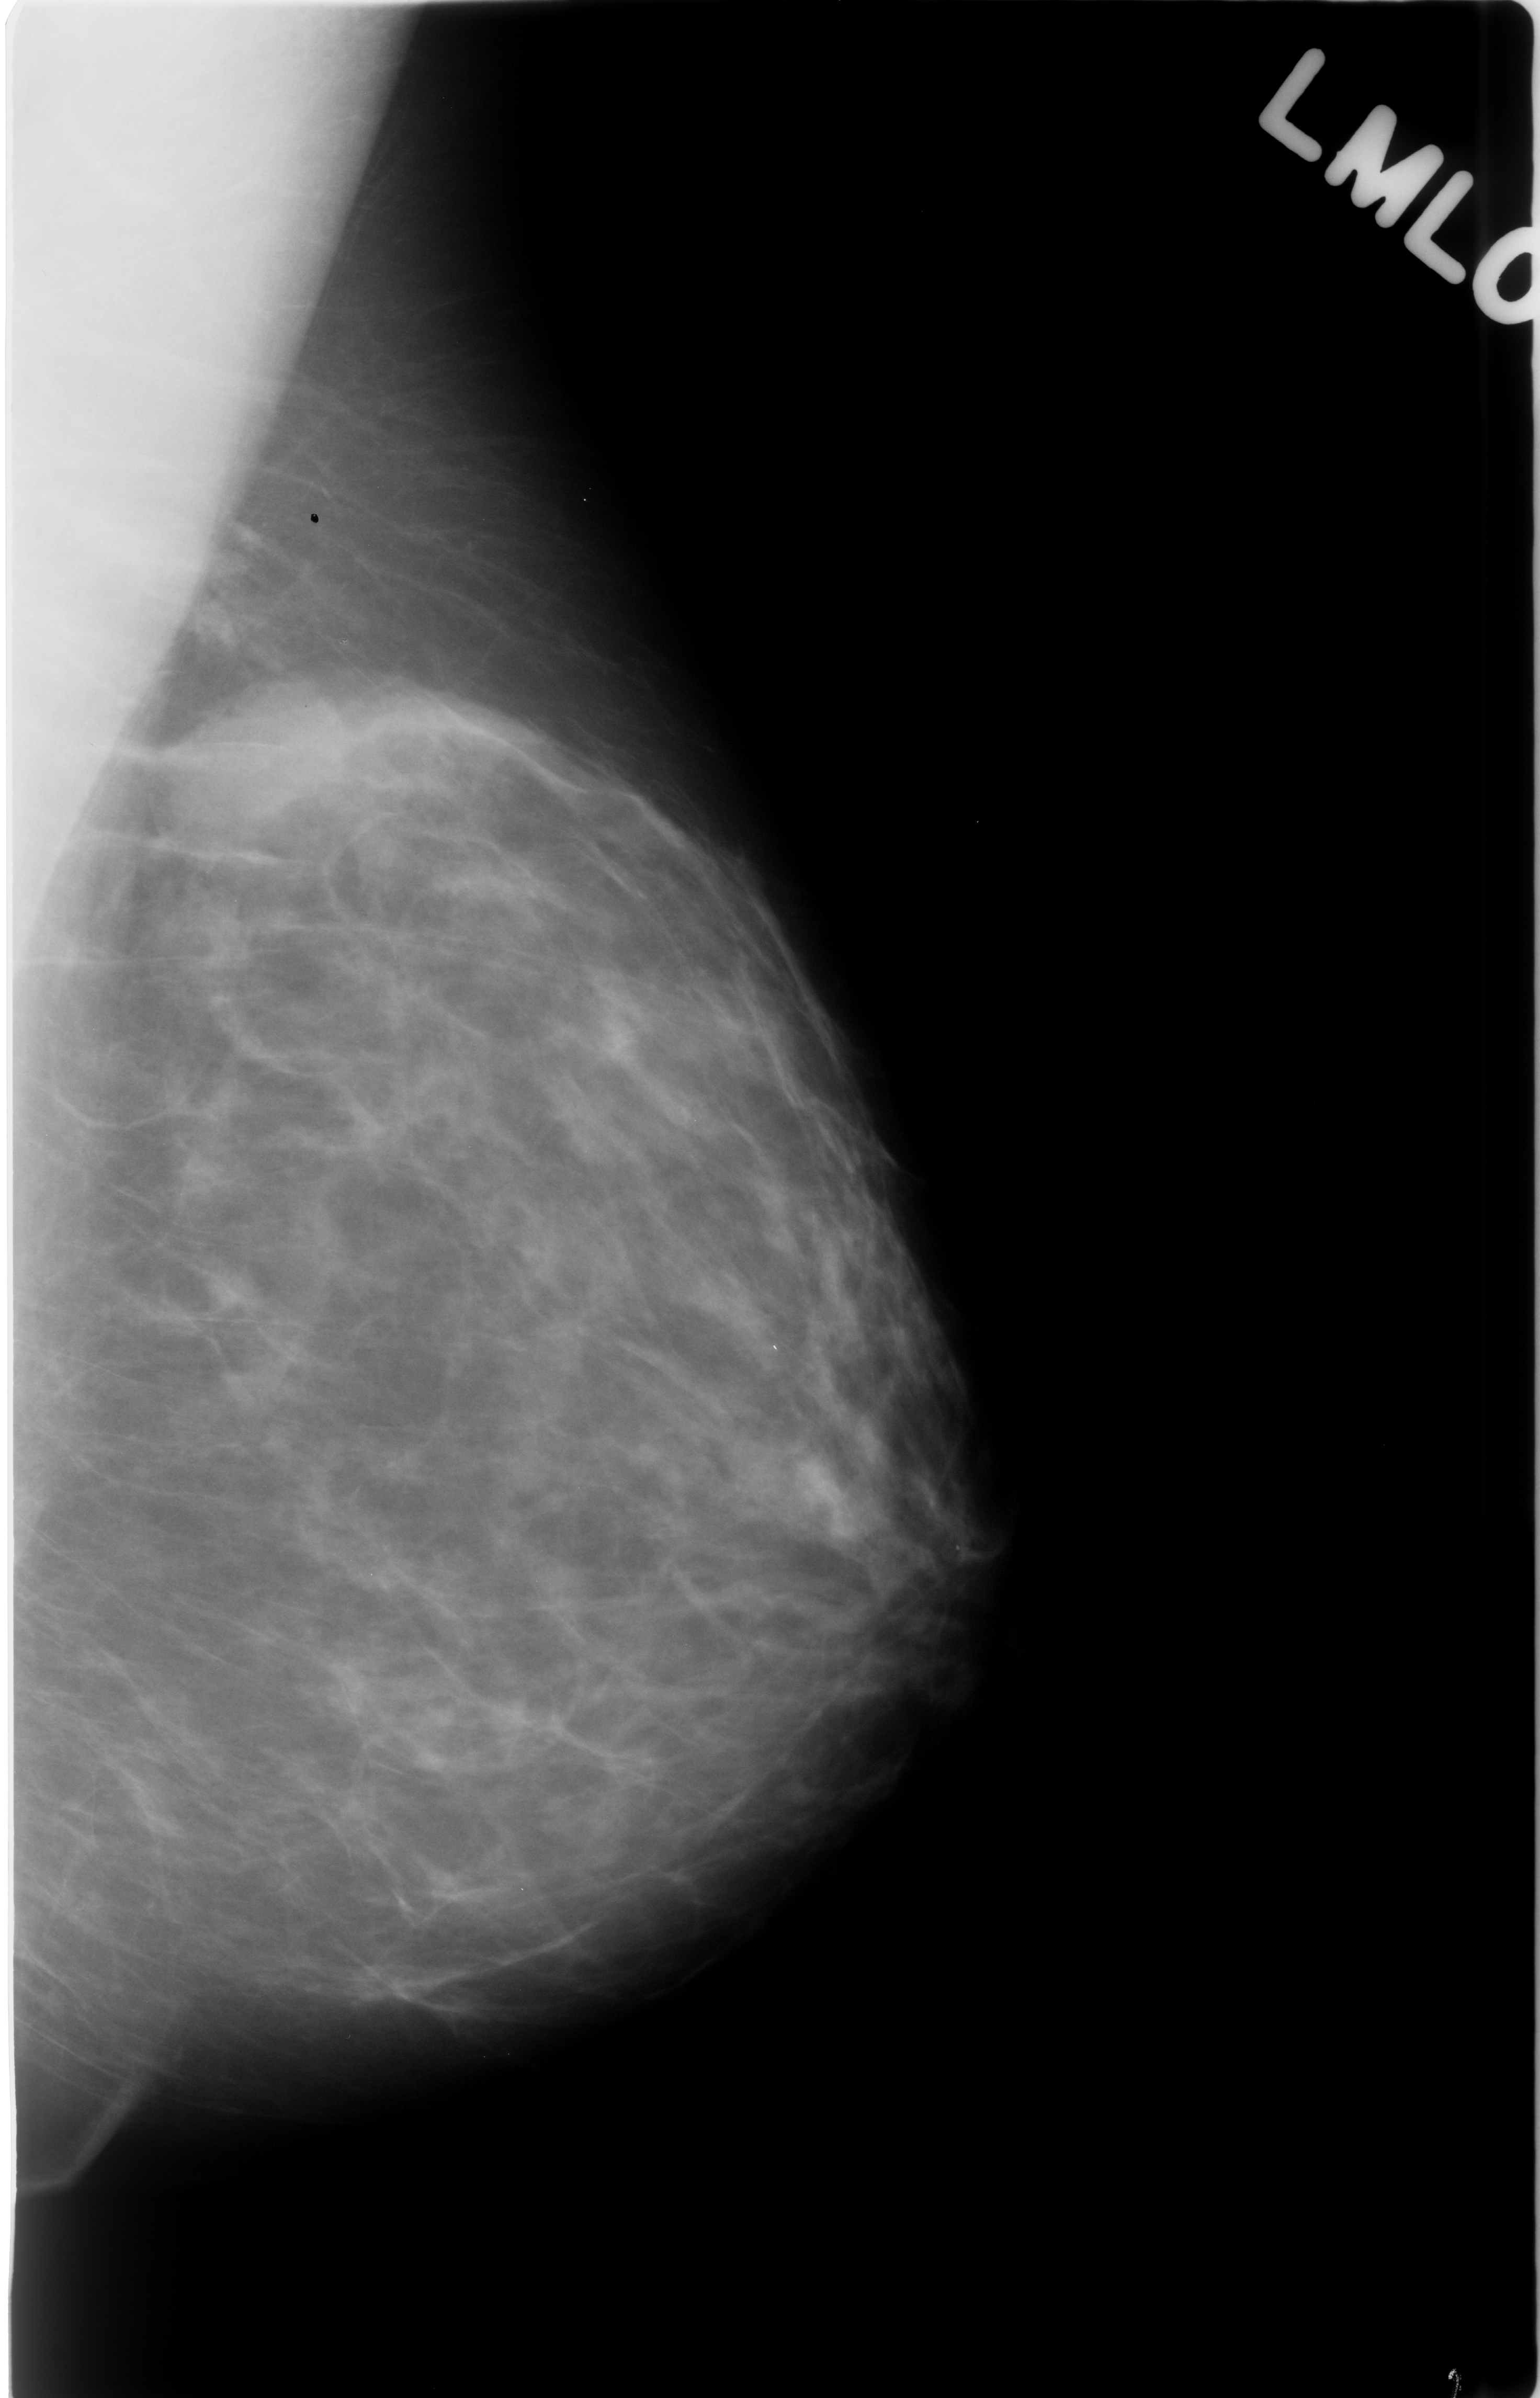
Mammogram (digitized film), left breast, MLO view, BI-RADS breast density category 1 (scale 1–4).
- Finding: mass, shape oval, margins ill defined; BI-RADS assessment category 3; subtlety rating 5 on a 1 (subtle) to 5 (obvious) scale; benign; no additional work-up was recommended (benign without callback).